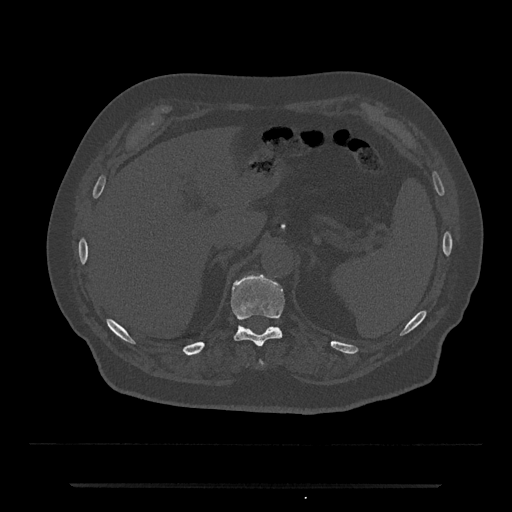
CT including the spine, one axial slice; position 647 of 797 along the scan axis; bone window (W 1800 / L 400 HU); 512 × 512 image matrix, field of view 434 × 434 mm. Male patient, age 80 years. From the clinical record (not read from this slice): primary cancer: prostate.
Outlined on this slice (semi-automatically segmented with operator editing):
- T11 vertebra: box from (x=230, y=275) to (x=285, y=347) px